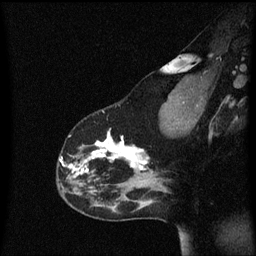
Breast MRI (dynamic contrast-enhanced), one sagittal slice; slice 42 of 60 in the series (ordered by position); dynamic contrast-enhanced series, image 2 of 3 at this slice position (ordered by acquisition); 1.5 T; TE 4.2 ms, TR 8.4 ms; 2 mm slice thickness; 256 × 256 image matrix, field of view 200 × 200 mm. Female patient, age 33 years.
Outlined on this slice (semi-automatically segmented with operator editing):
- analysis volume of interest (the breast-tissue region the enhancement analysis was run in; not a lesion): box from (x=57, y=122) to (x=152, y=191) px
- tumour enhancement mask (voxels above the 70 % enhancement threshold inside the analysis volume of interest): (x=60, y=130)–(x=151, y=175)